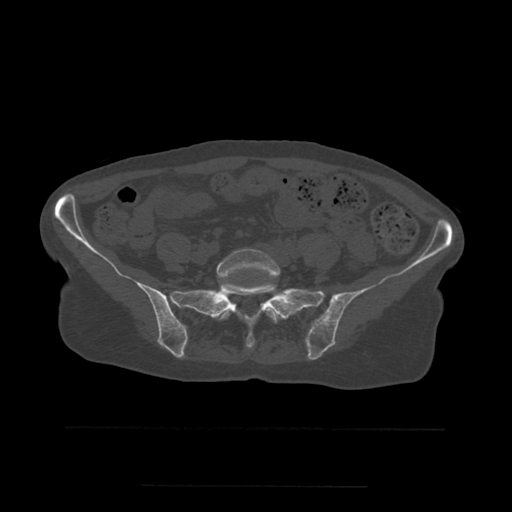
CT including the spine, one axial slice. Bone window (W 1800 / L 400 HU). 1.25 mm slice thickness. 512 × 512 image matrix, field of view 350 × 350 mm. Patient age 58 years. From the clinical record (not read from this slice): primary cancer: lung.
Outlined on this slice (semi-automatic segmentation, software-assisted and operator-edited):
- L5 vertebra: box from (x=217, y=249) to (x=280, y=324) px